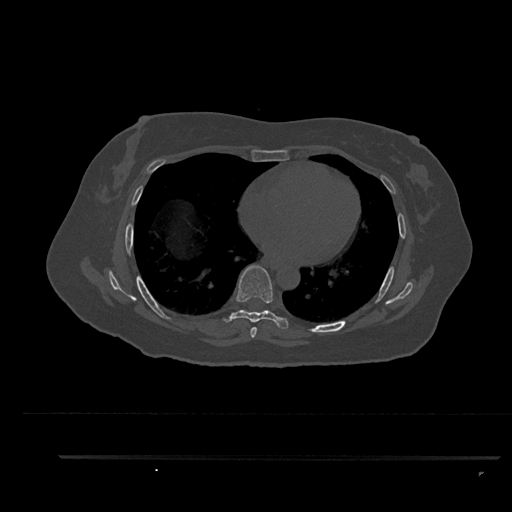
CT including the spine, one axial slice. Slice 510 of 797 in the series (ordered by position). Reconstruction kernel Br40s/3. Bone window (W 1800 / L 400 HU). 512 × 512 image matrix, field of view 408 × 408 mm. Patient: female, 44 years. Case-level facts recorded for this patient, not image findings: primary cancer: renal; vertebrae with lytic lesions (as recorded): L1.
Outlined on this slice (semi-automatically segmented with operator editing):
- T6 vertebra: bounding box [x1, y1, x2, y2] px = [250, 327, 257, 338]
- T7 vertebra: [222, 265, 289, 329]